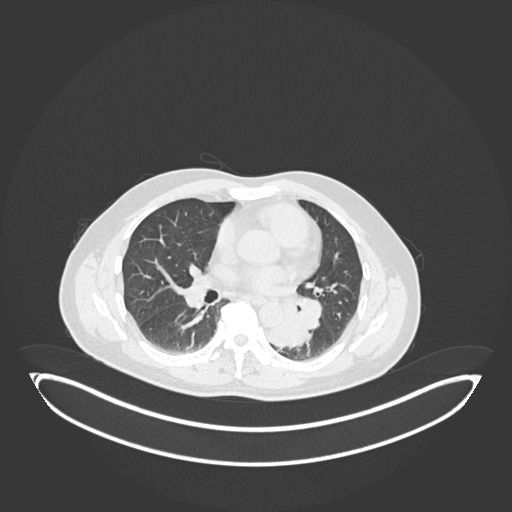
Chest CT, one axial slice; position 99 of 258 along the scan axis; reconstruction kernel B30f; 120 kVp; lung window (W 1500 / L -600 HU); 1 mm slice thickness; 512 × 512 image matrix, field of view 500 × 500 mm. Male patient, age 54 years. Case-level facts recorded for this patient, not image findings: clinical TNM (as recorded): T3 N0 M0.
Structures marked on this image (rectangle marked by the reading radiologist):
- lung tumour (recorded histology: squamous cell carcinoma): bounding box <263,300,310,350> (left, top, right, bottom; pixels)